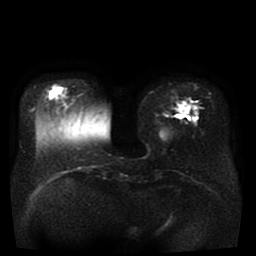
Breast MRI, one axial slice; position 10 of 41 along the scan axis; diffusion-weighted series; image 2 of 4 stored at this slice position (different b-values; order by instance number); 1.5 T; 5 mm slice thickness; 256 × 256 image matrix, field of view 330 × 330 mm. Female patient.
Structures marked on this image (outlined manually by an expert reader):
- tumour on diffusion-weighted imaging: bounding box <176,102,189,115> (left, top, right, bottom; pixels)